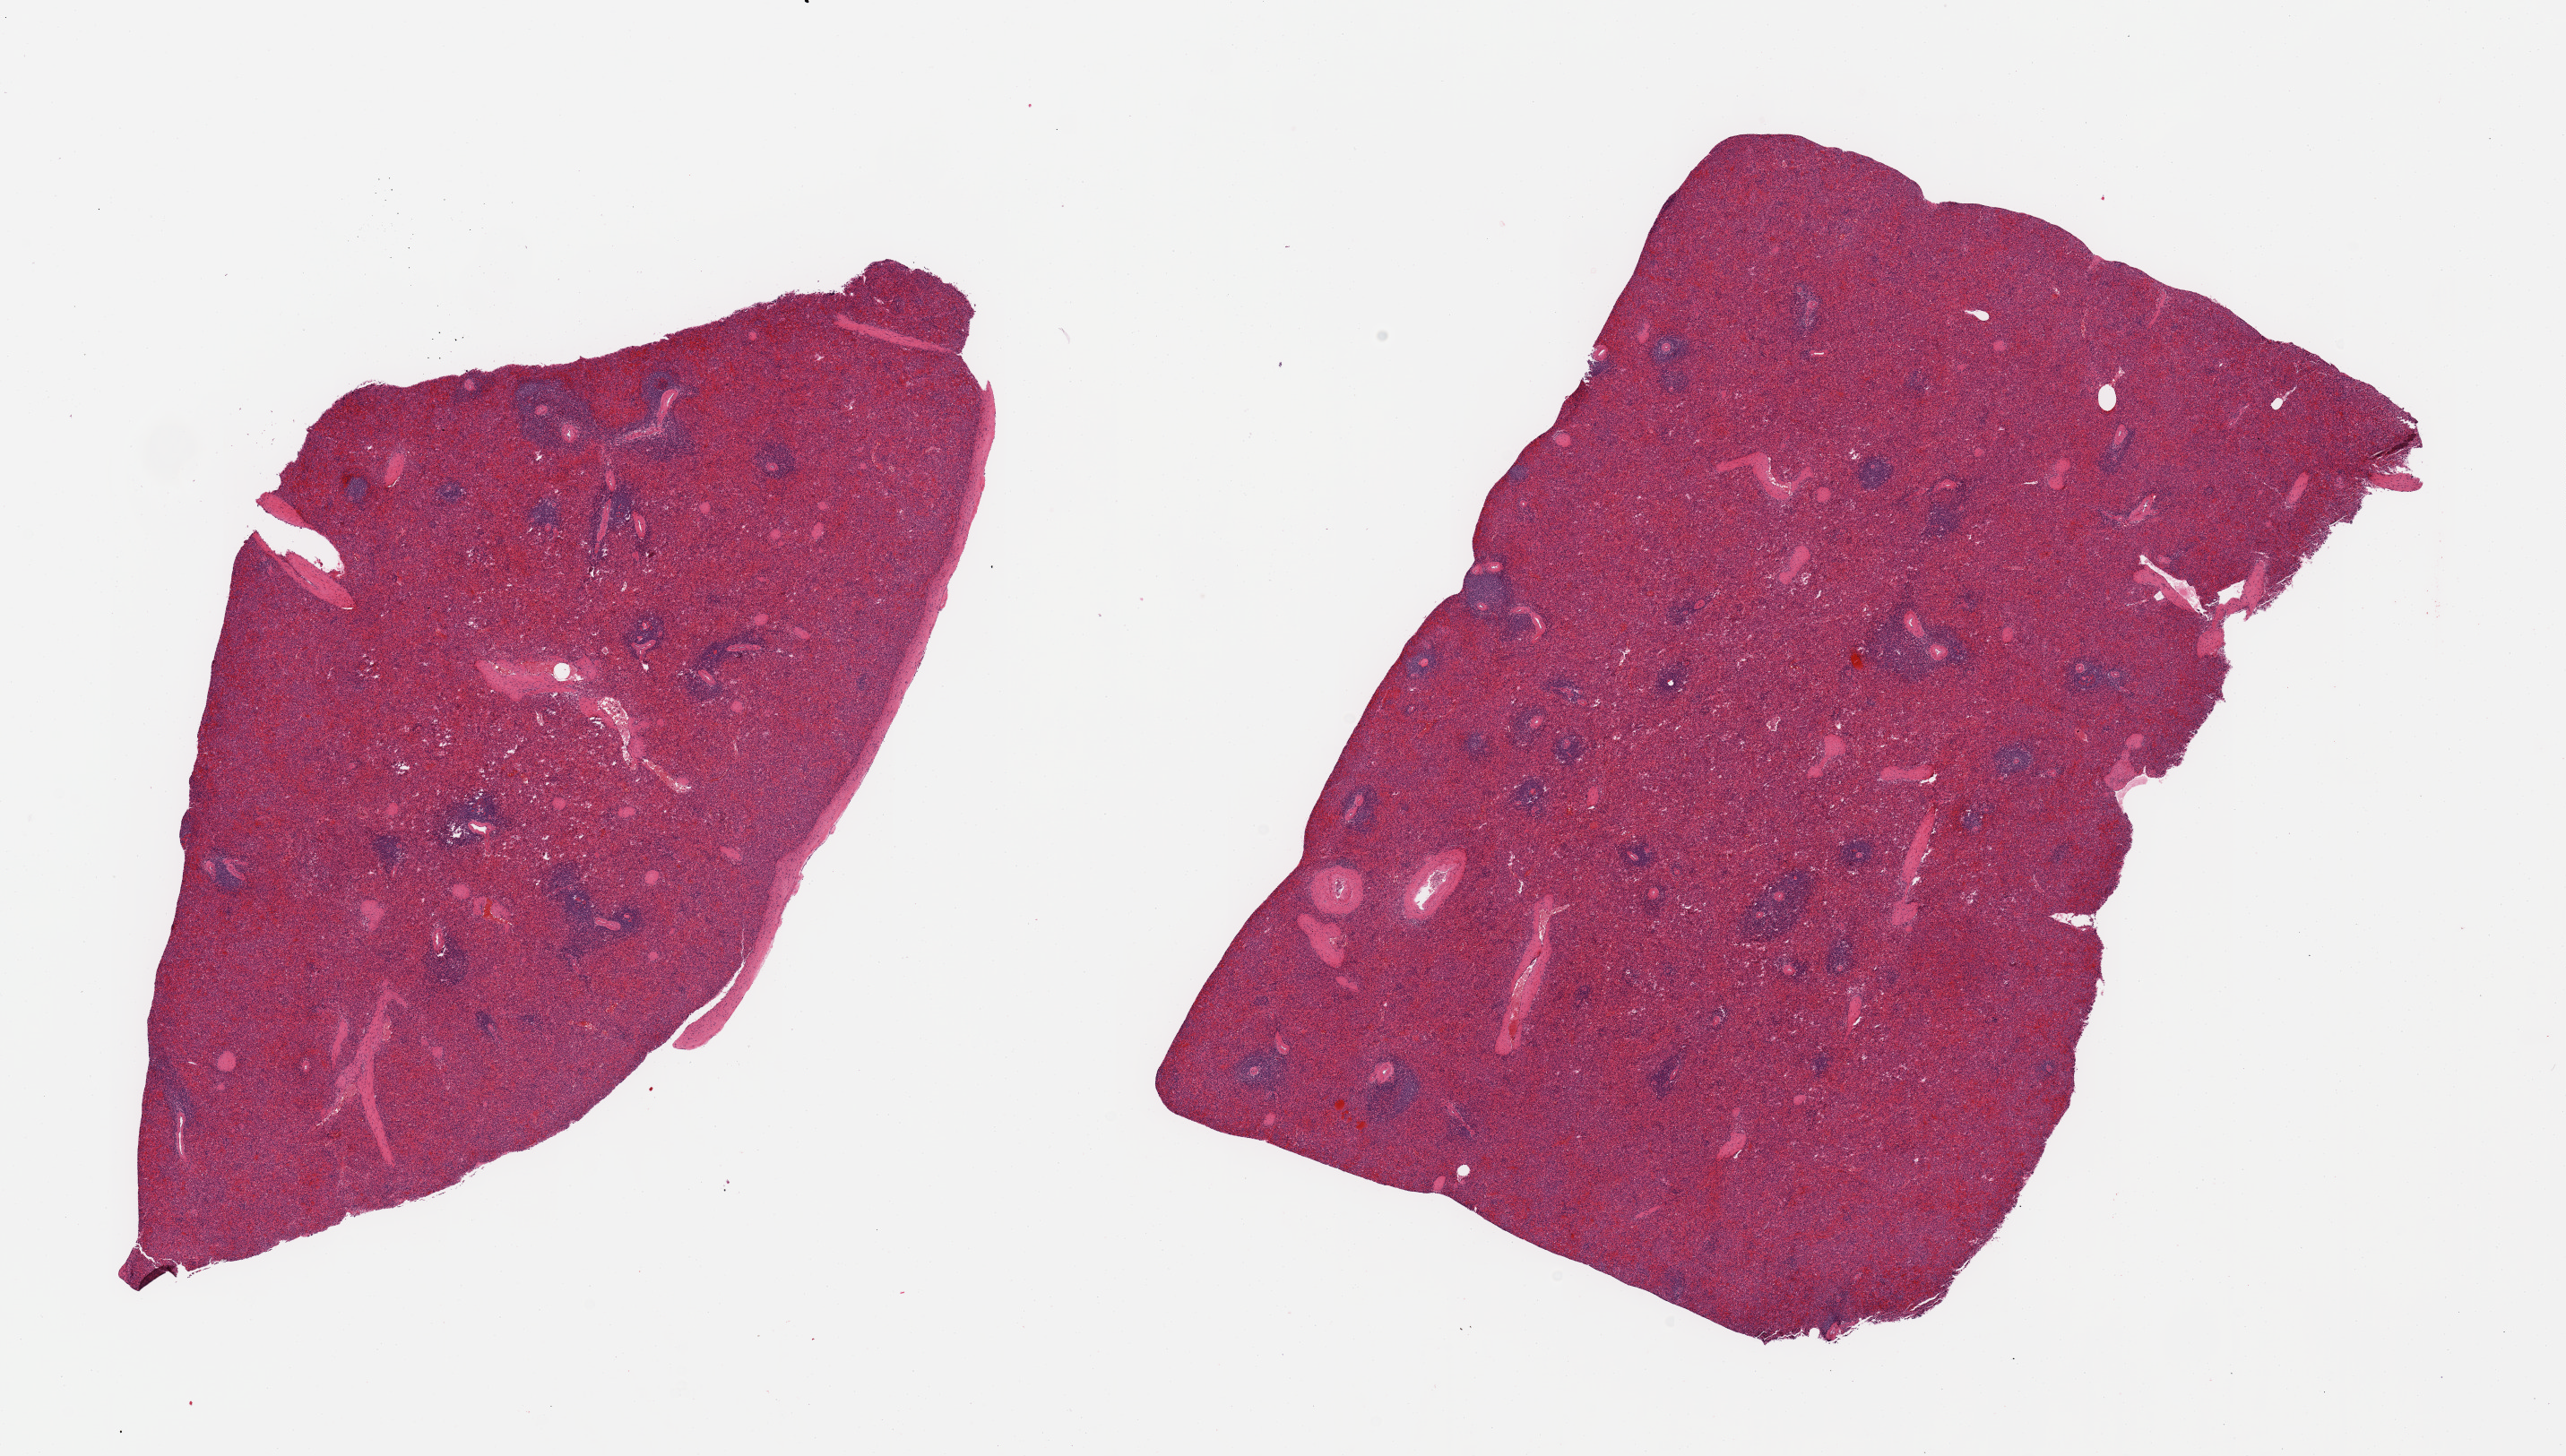
Digitized haematoxylin and eosin-stained section, brightfield, low-resolution overview of the scanned area, about 22.6 x 12.9 mm. PAXgene-fixed paraffin-embedded (PFPE) section. Section of spleen (target tissue). Donor tissue sample.
Pathologist's review note for this sample: 2 pieces; capsule present on 1 piece (target is 5mm below capsule).